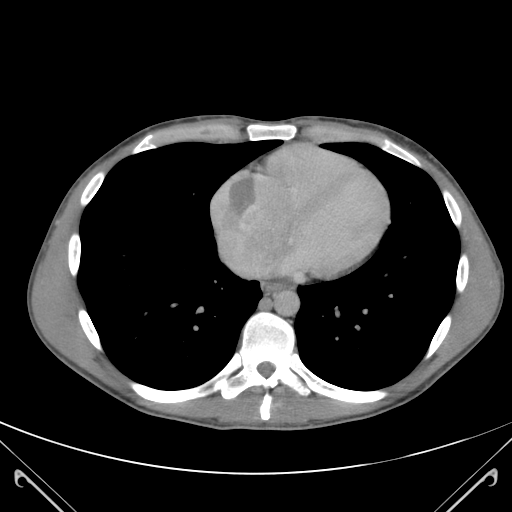
Contrast-enhanced abdominal CT (liver protocol), one axial slice. Position 116 of 118 along the scan axis. Soft-tissue window (W 400 / L 40 HU). 3 mm slice thickness. 512 × 512 image matrix, field of view 380 × 380 mm. Case-level facts recorded for this patient, not image findings: diagnosis: hepatocellular carcinoma (patient treated with transarterial chemoembolisation; whether this scan precedes or follows treatment is not stated here); TNM stage (as recorded): Stage-IIIB; Child-Pugh class: A; tumour nodularity: uninodular.
Outlined on this slice (semi-automatically segmented with operator editing):
- abdominal aorta: bounding box (x1, y1, x2, y2) in pixels: (274, 290, 298, 314)